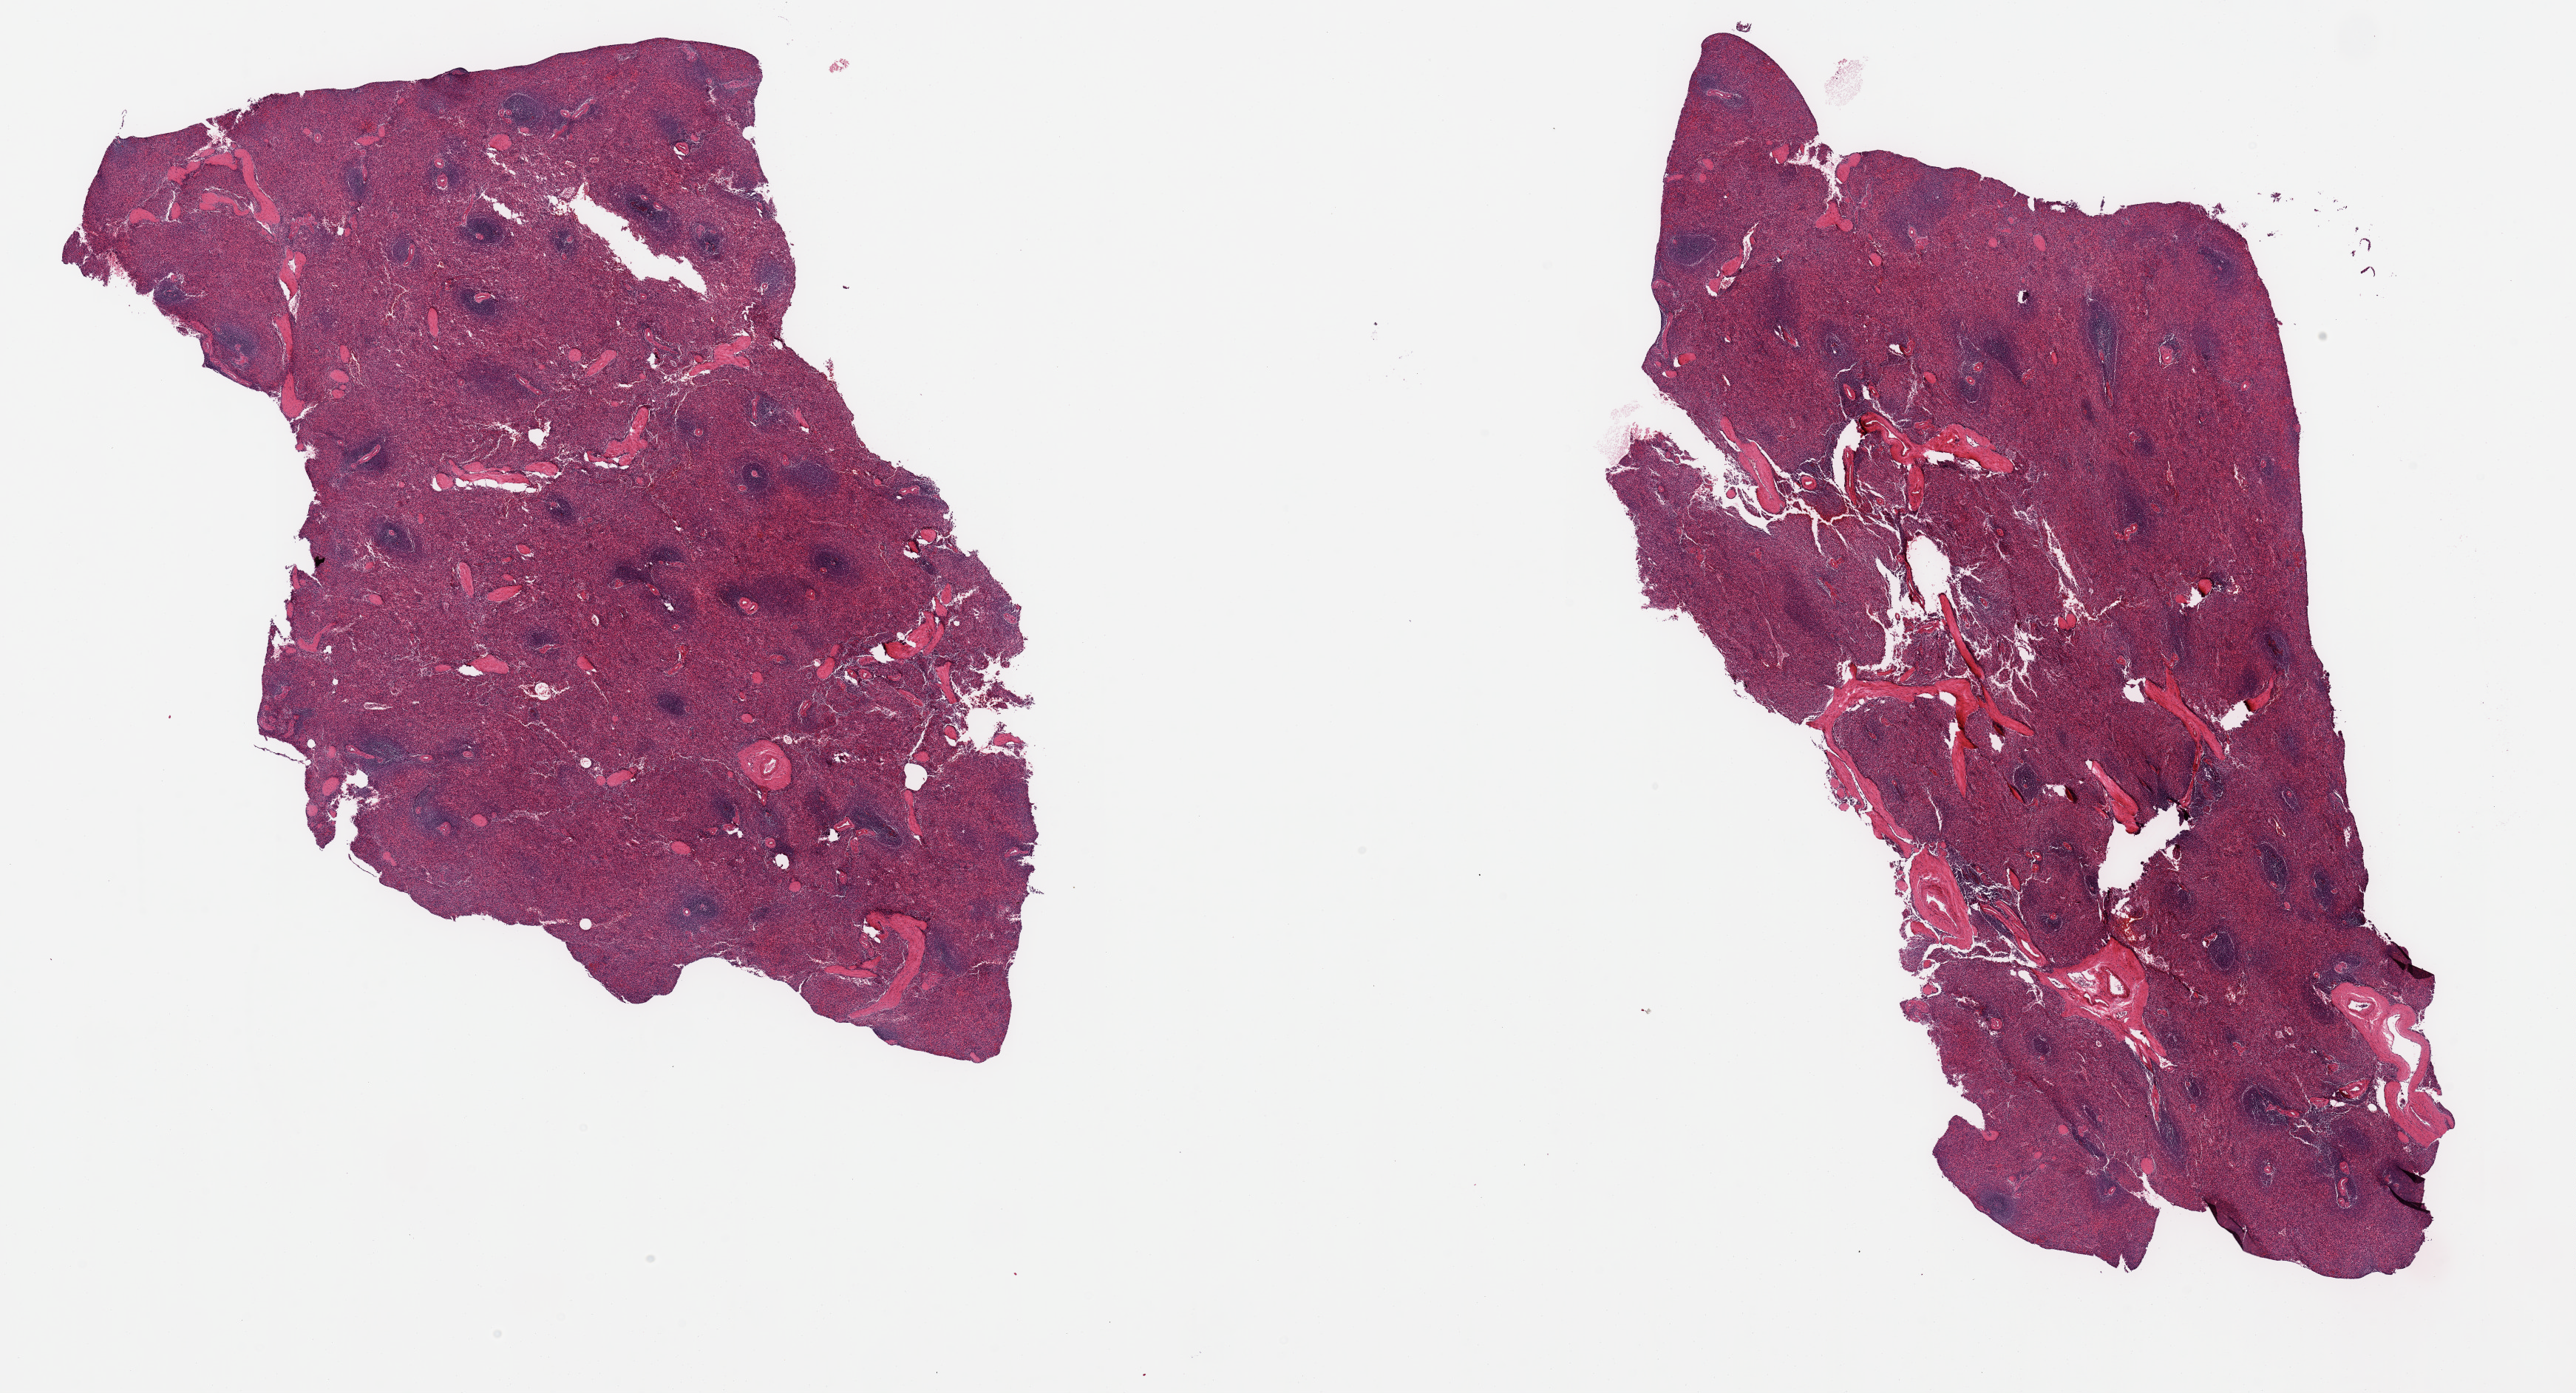
Haematoxylin and eosin whole-slide image — shown as a low-resolution overview of the whole scanned area (about 27.6 x 14.9 mm). PAXgene-fixed, paraffin-embedded tissue. Sampled site (target tissue): spleen. Tissue donor sample. Female donor.
• review note (as recorded): 2 pieces